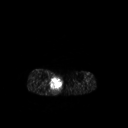
FDG PET of an extremity soft-tissue mass (from a PET/CT study), one axial slice. Position 130 of 267 along the scan axis. 3.27 mm slice thickness. 128 × 128 image matrix, field of view 500 × 500 mm. Male patient, age 69 years. From the clinical record (not read from this slice): histological type: pleiomorphic liposarcoma; grade: high; site of the primary tumour: right calf.
Annotated regions visible in this slice (expert contour drawn on MRI and transferred to this co-registered scan by the dataset authors):
- gross tumour volume including surrounding oedema: box from (x=49, y=75) to (x=63, y=95) px
- gross tumour volume (mass): (x=50, y=76)–(x=63, y=89)